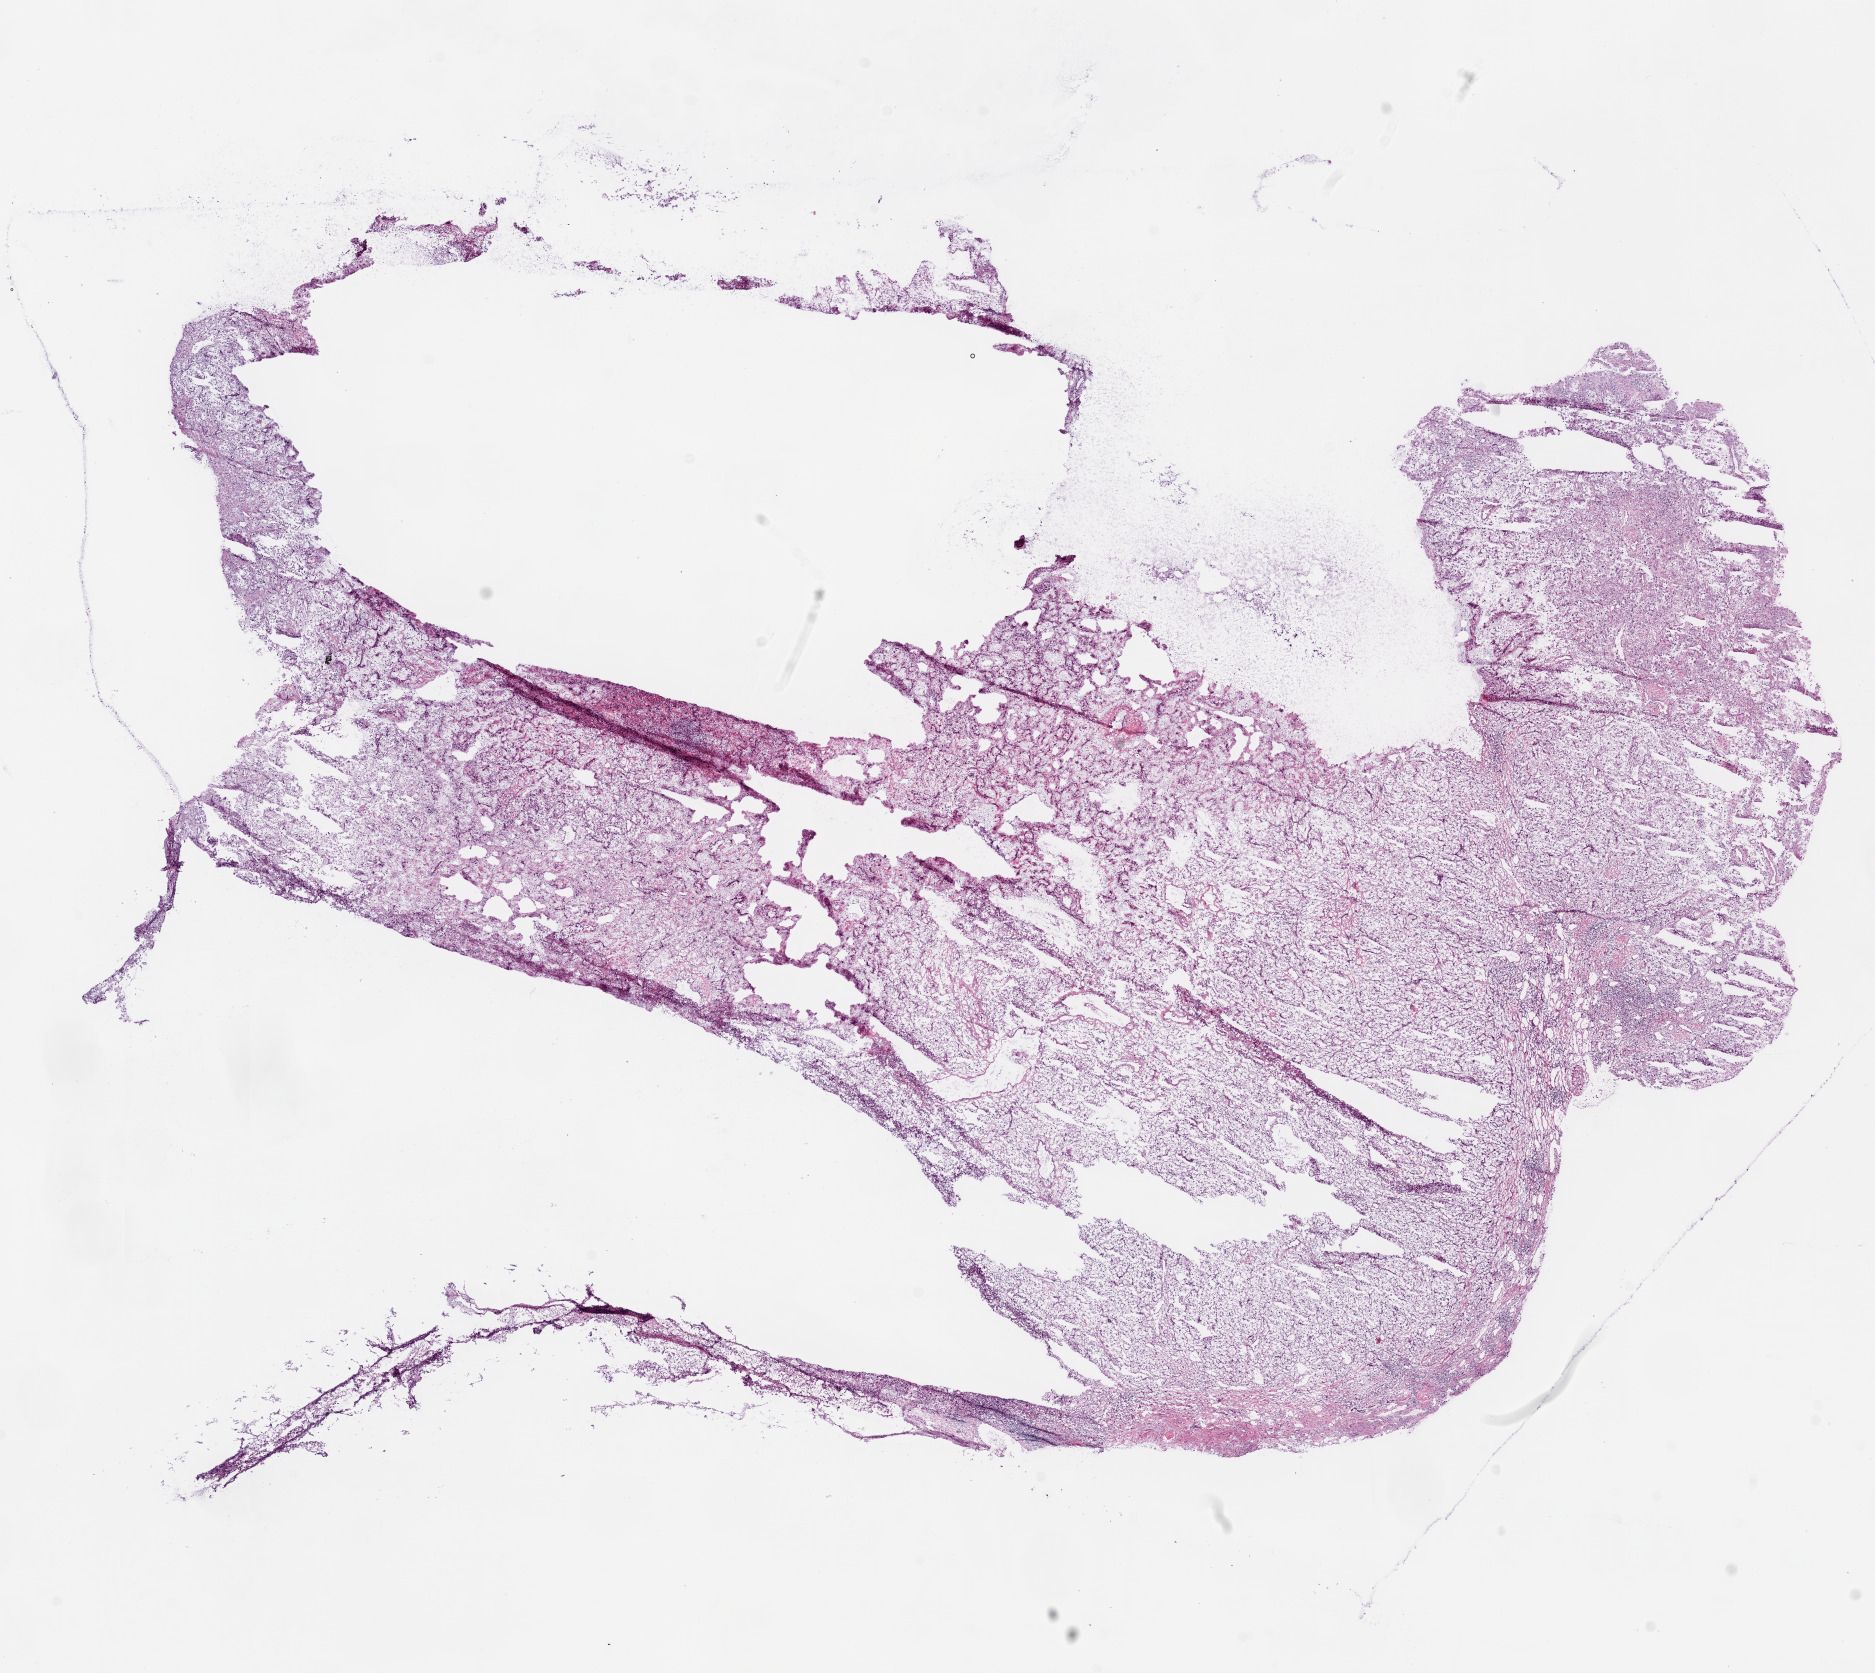
Hematoxylin and eosin (H&E) stained whole-slide image, shown as a low-resolution overview of the whole scanned area (about 15.0 x 13.4 mm), frozen section, primary tumour sample from the kidney. Male patient; age at initial diagnosis 64 years. Histologic grade: G3 (poorly differentiated). Composition of this section per pathologist review: tumour cells 90%, tumour nuclei 80%, normal cells 0%, stromal cells 10%, necrosis 0%.
Diagnosis: Clear cell adenocarcinoma, NOS. Lymph nodes positive (case pathology): 0 of 7 examined. AJCC pathologic stage: III. TNM: T3a N0 M0.